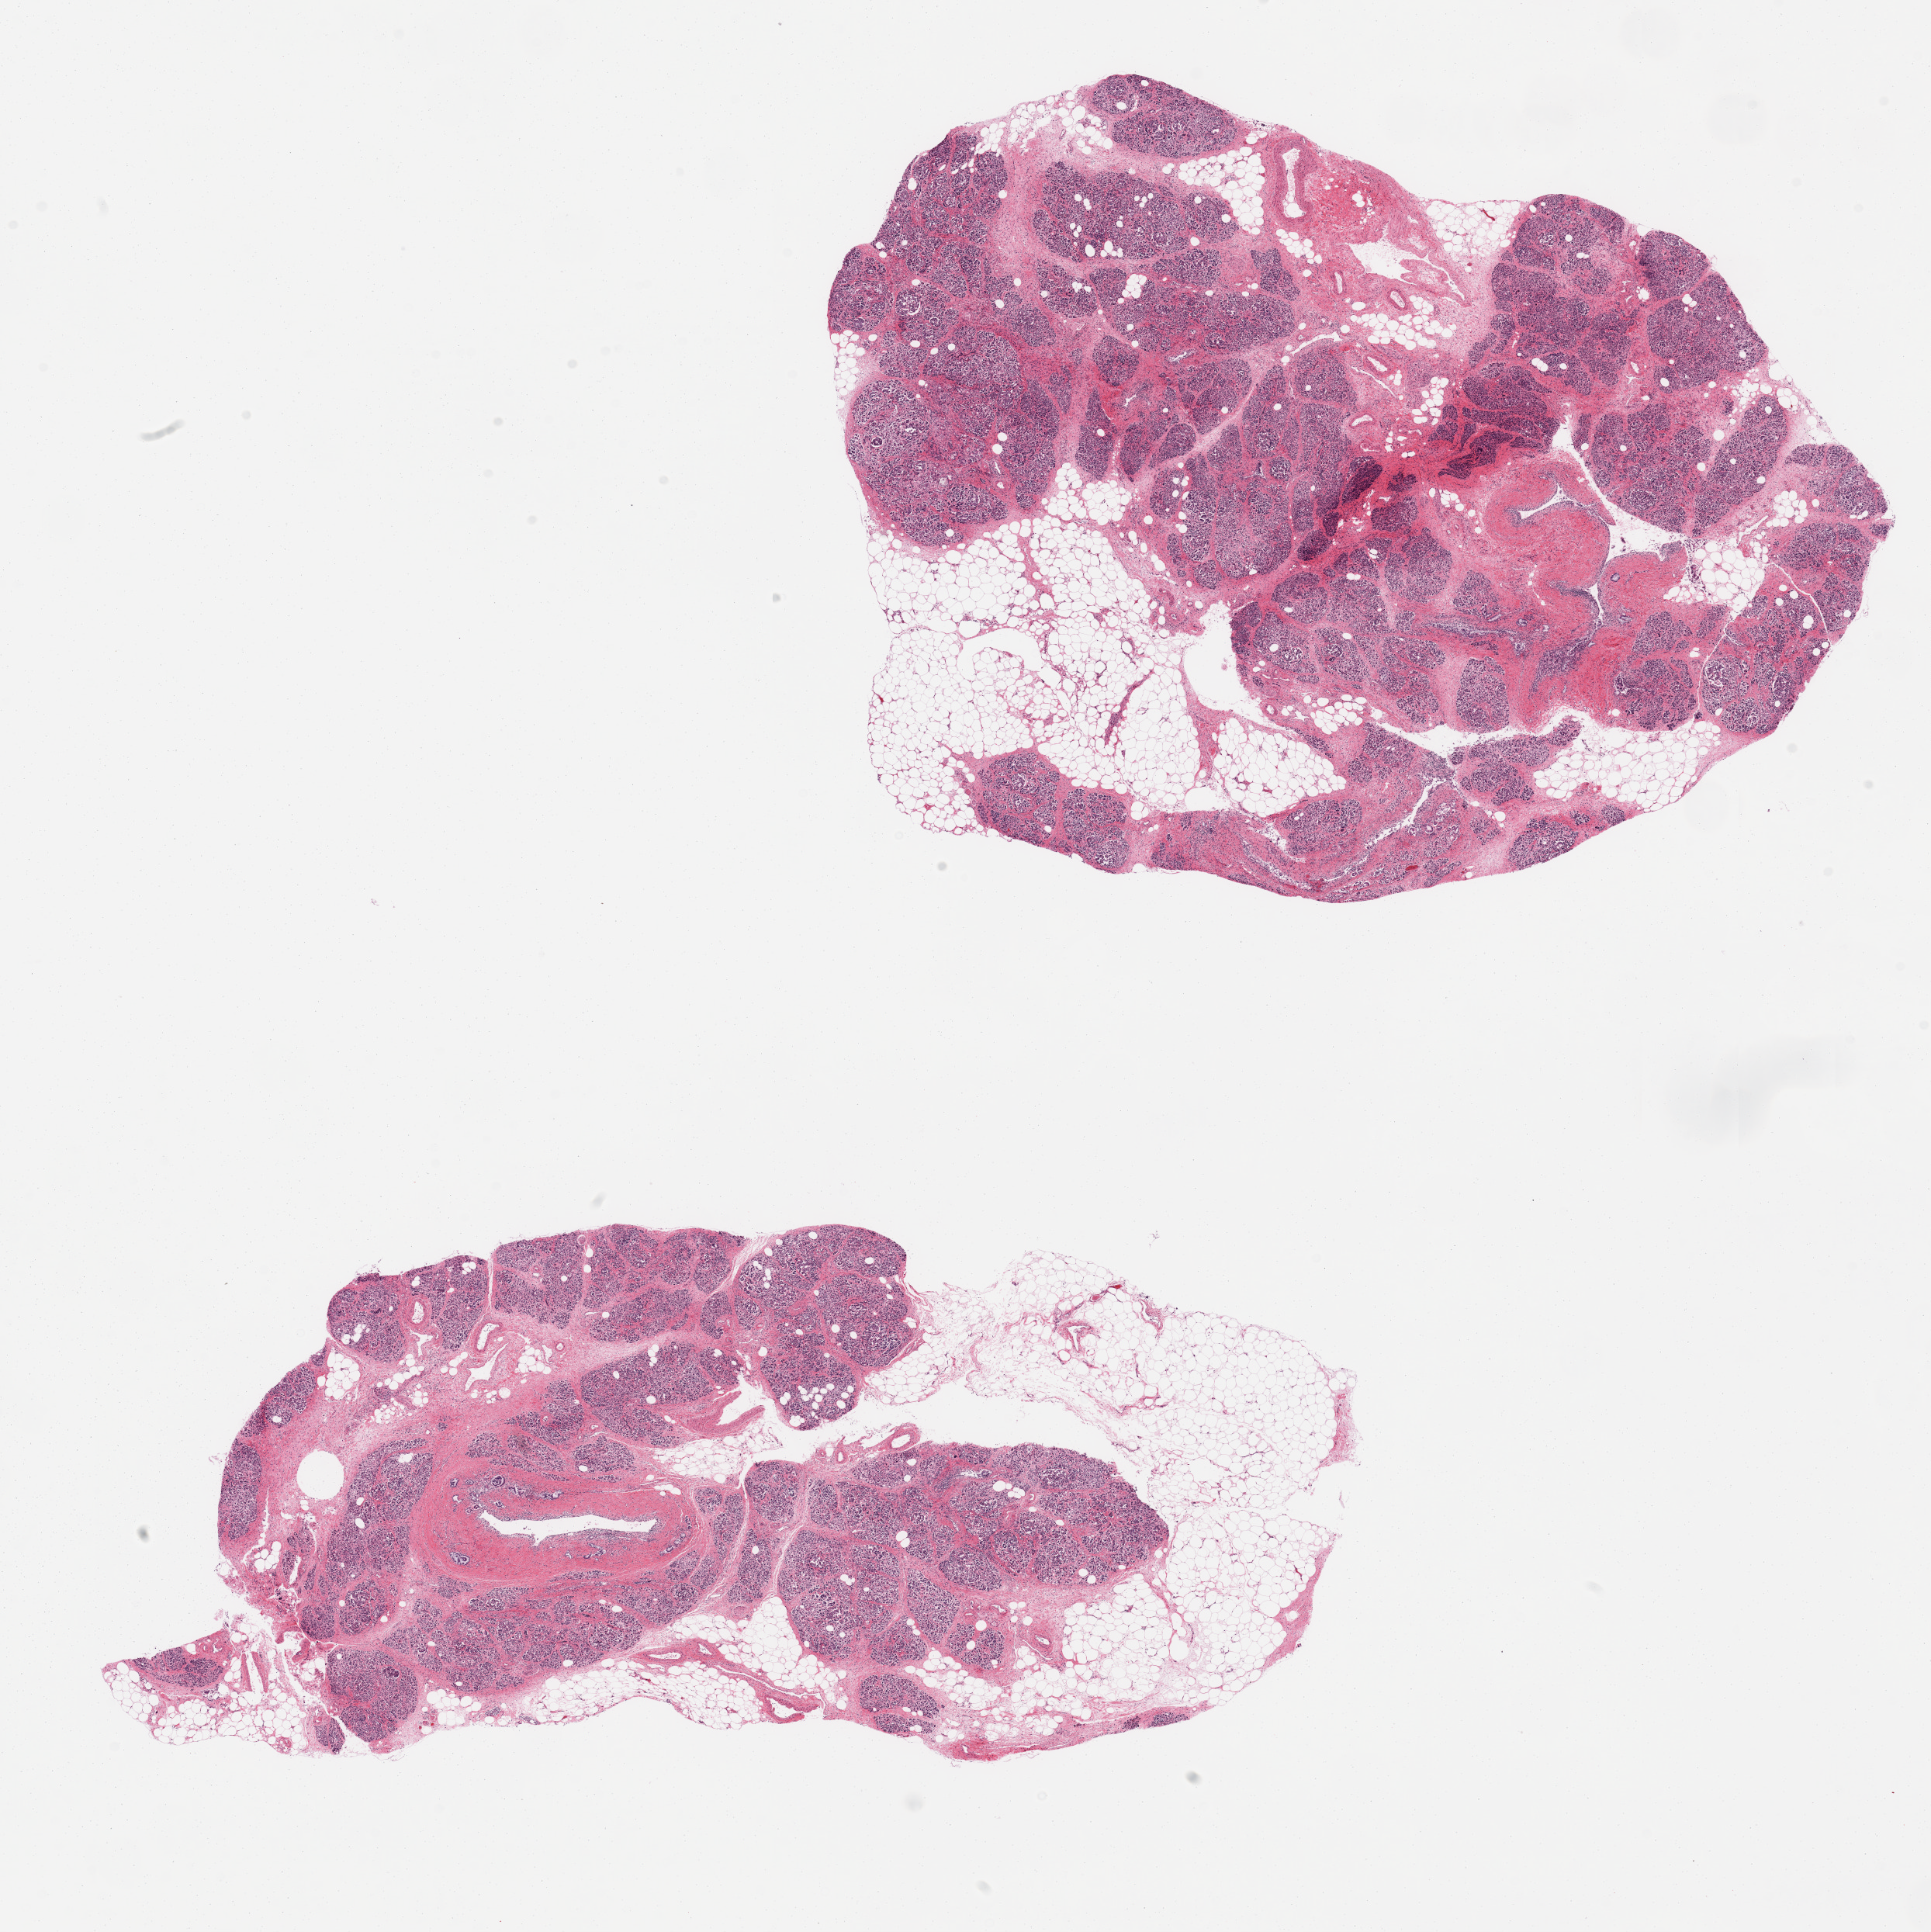
Whole-slide image, haematoxylin and eosin stain — low-resolution overview of the scanned area, about 19.7 x 19.7 mm. PAXgene-fixed, paraffin-embedded tissue. Target tissue: pancreas. Tissue donor sample. Male donor.
Reviewer comment on this tissue sample: 2 pieces.